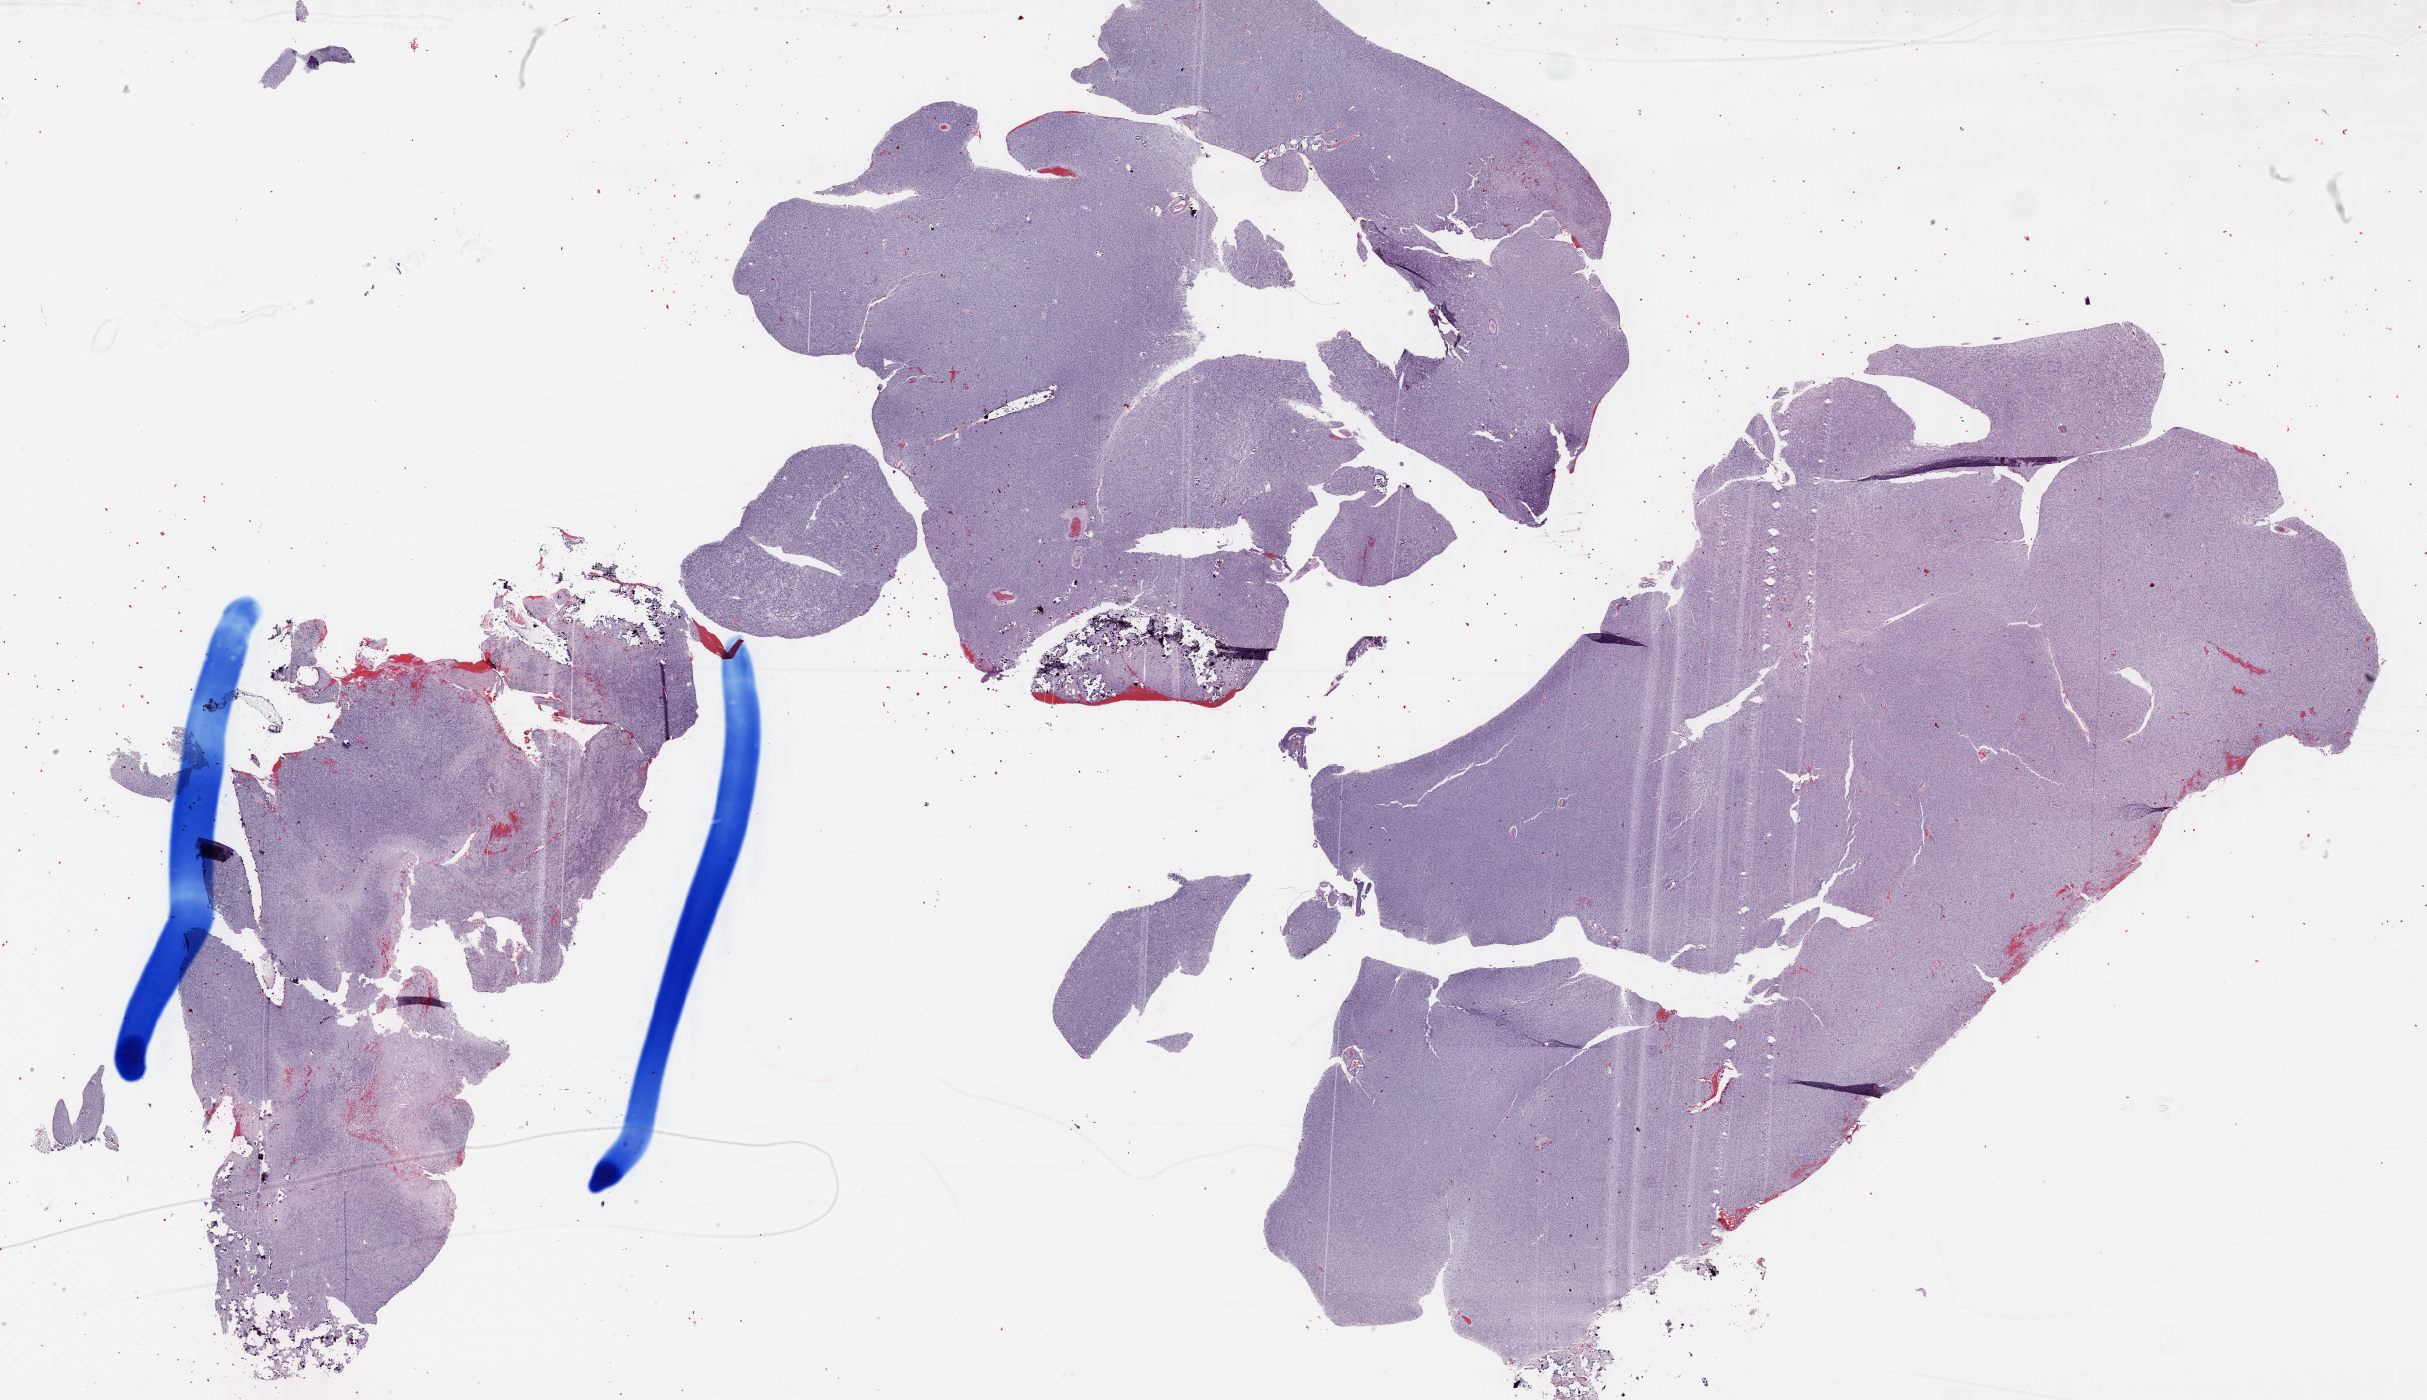
Hematoxylin and eosin (H&E) stained whole-slide image — a low-resolution overview of the entire scanned area, about 39.2 x 22.6 mm; FFPE section; sample: primary tumour, brain. Male, age 26 years at initial diagnosis.
Histologic diagnosis: Mixed glioma (cerebrum).